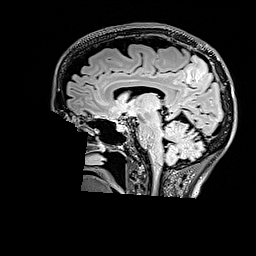
Brain MRI from a brain-tumour surgery series, one sagittal slice. Position 97 of 176 along the scan axis. T2 FLAIR. 1 mm slice thickness. 256 × 256 image matrix, field of view 256 × 256 mm. Case-level facts recorded for this patient, not image findings: histopathology: Astrocytoma; WHO grade: 3; IDH mutation: yes; tumour location: Right Parietal.
Outlined on this slice (manually delineated by an expert):
- tumour: box from (x=183, y=57) to (x=207, y=82) px
- tumour: (x=184, y=55)–(x=213, y=82)